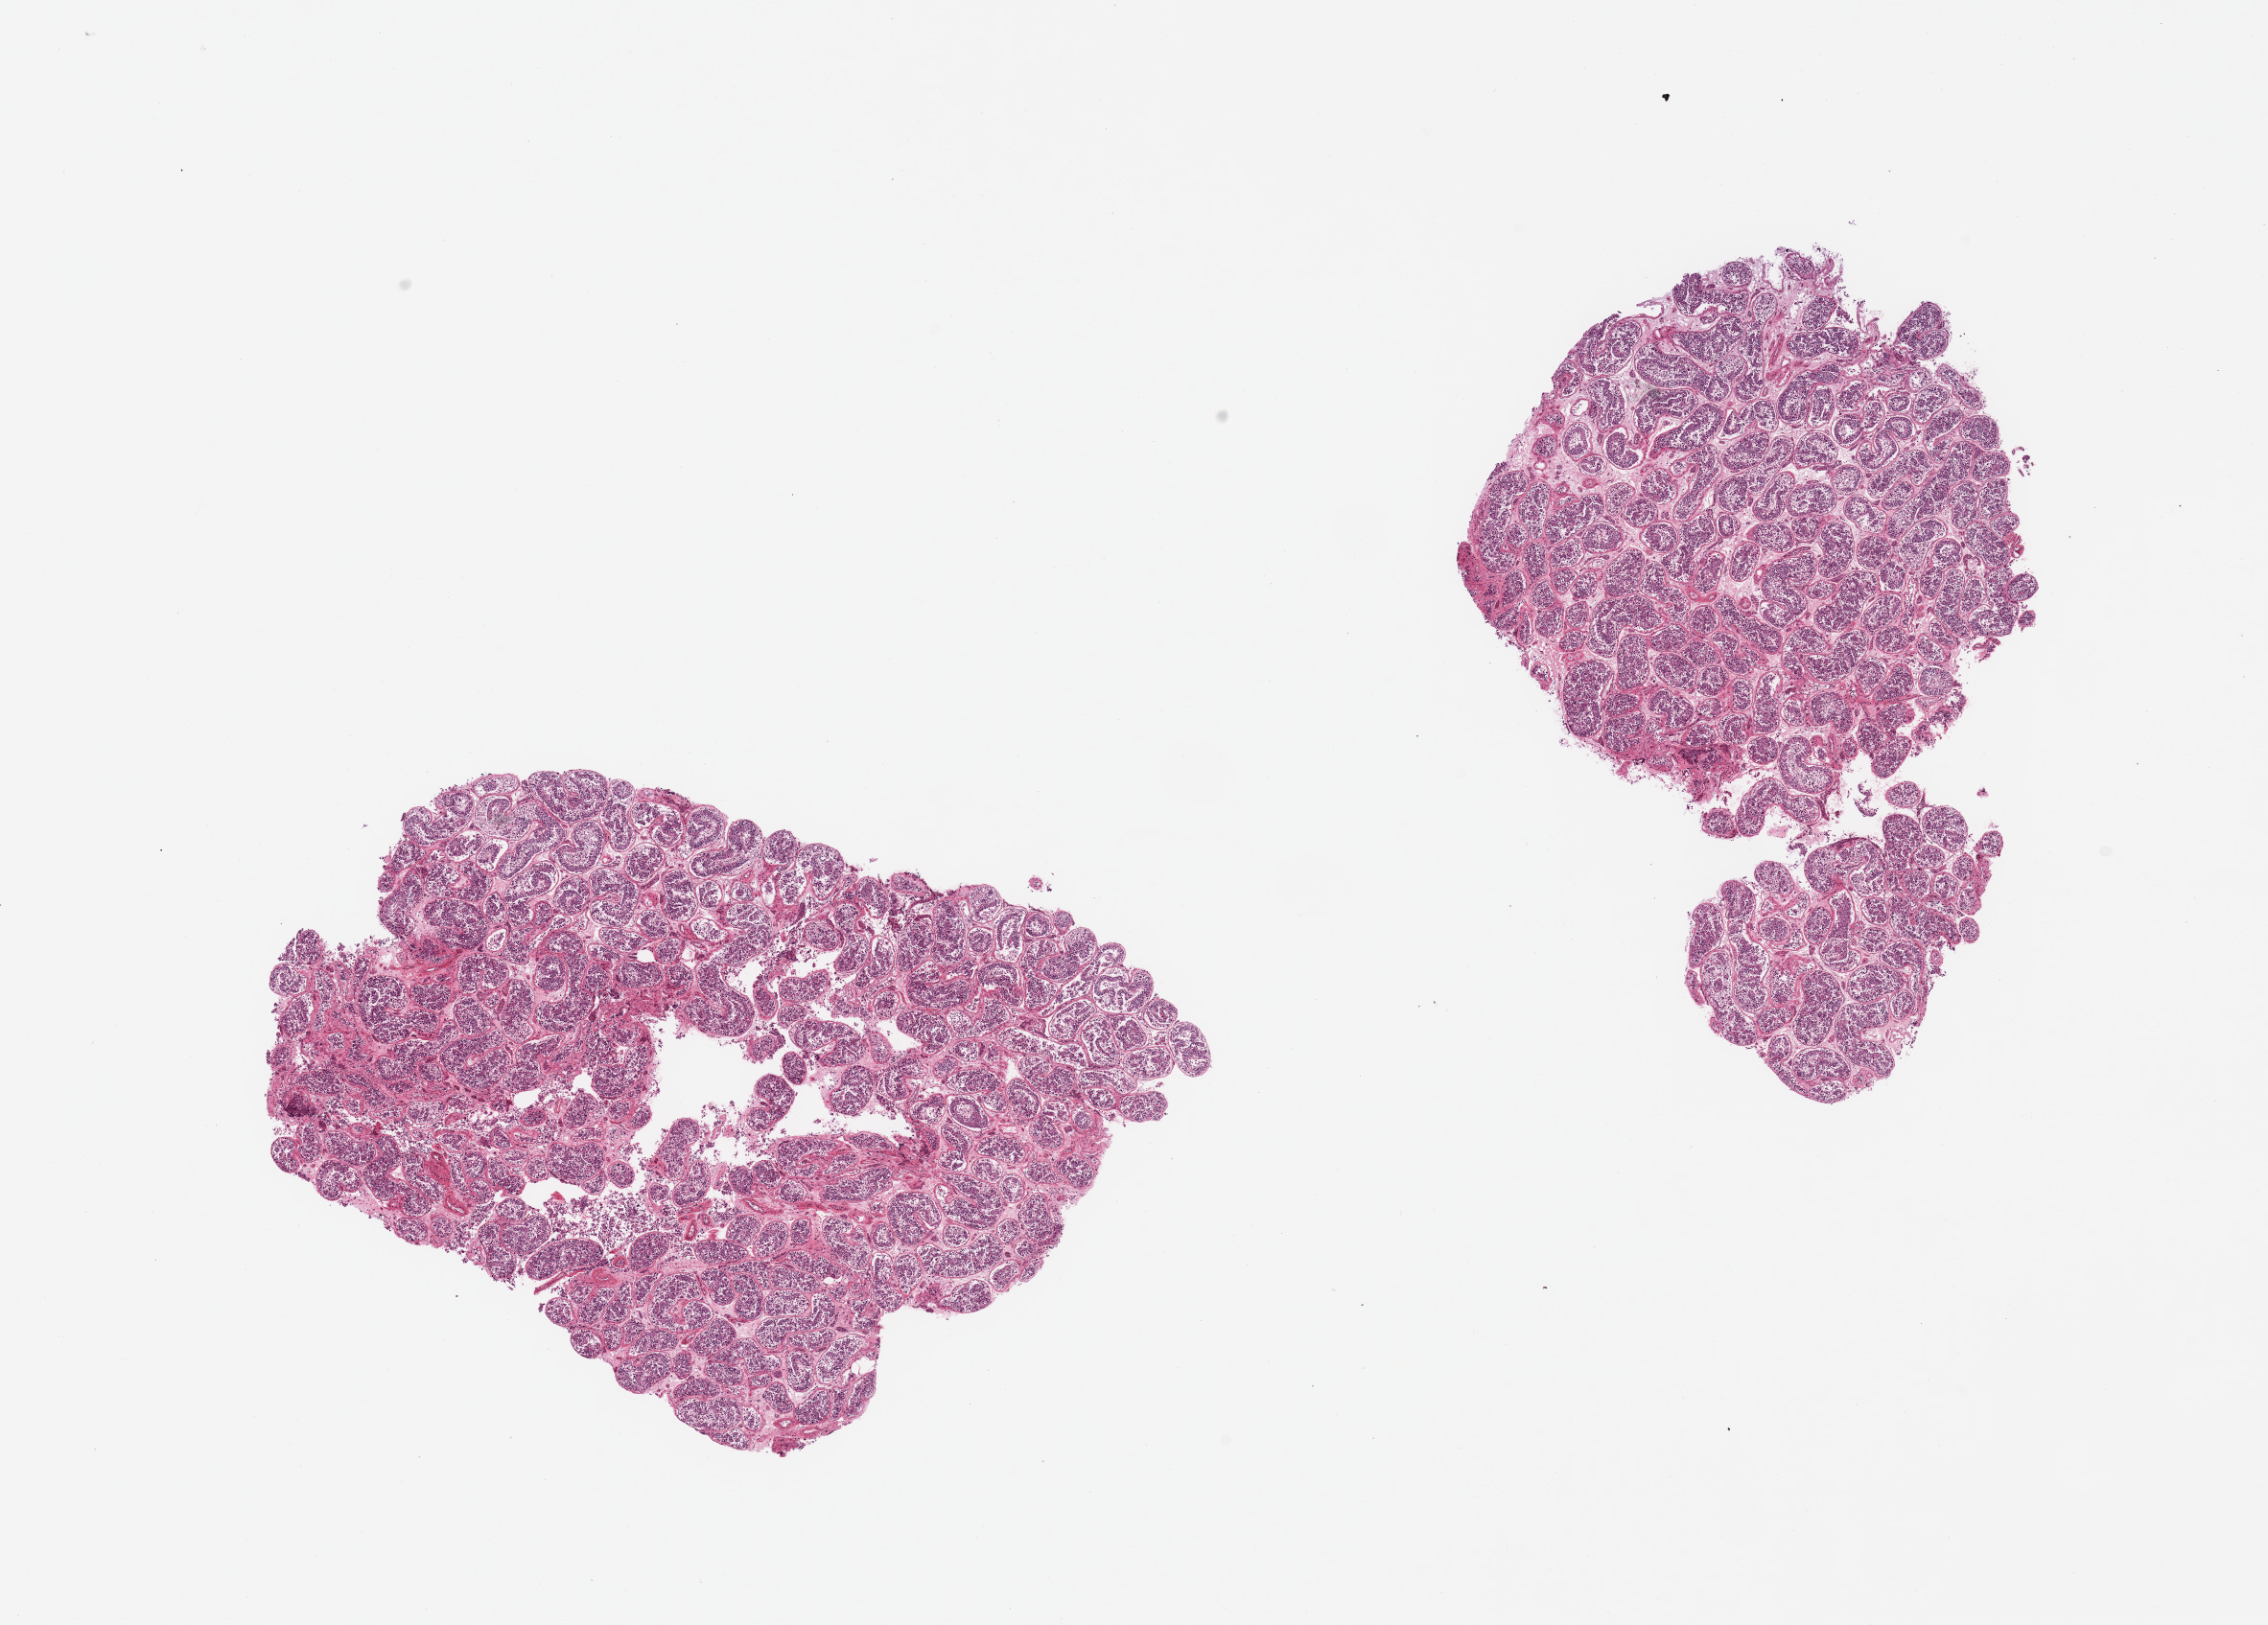
Whole-slide image, hematoxylin and eosin (H&E) stain, brightfield — low-resolution overview of the scanned area, about 18.7 x 13.4 mm. PAXgene-fixed, paraffin-embedded tissue. Section of testis (target tissue). Tissue donor sample.
Pathologist's review note for this sample: 2 pieces; active spermatogenesis.